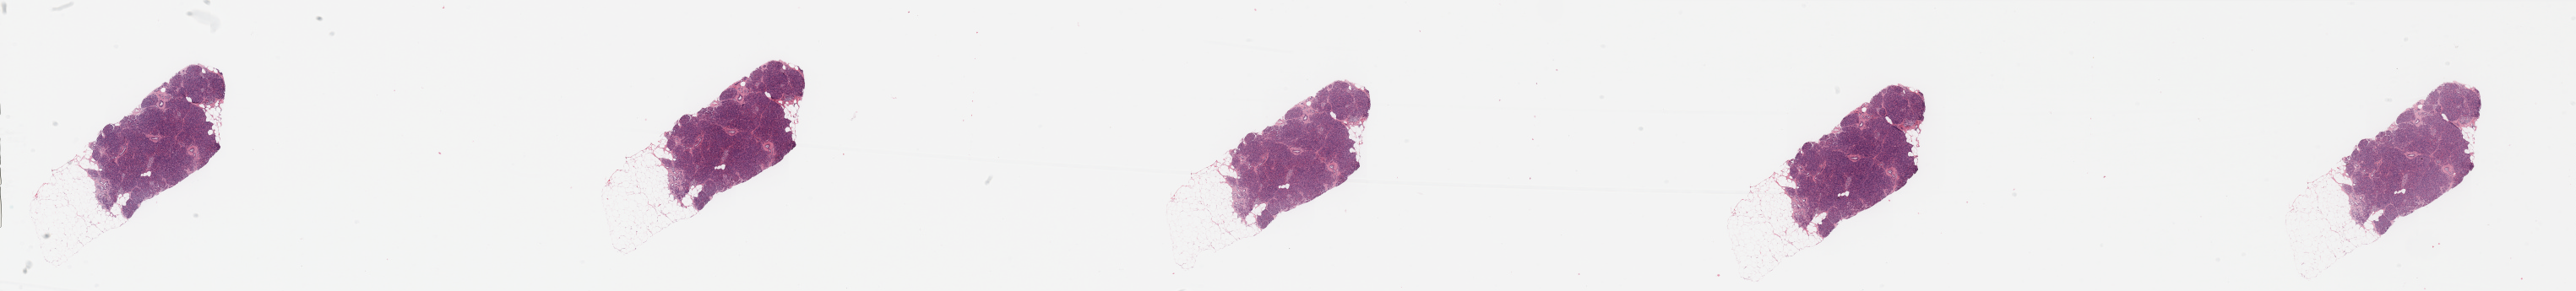
Digitized Hematoxylin and eosin (H&E) stained tissue section (whole slide), shown as a low-resolution overview of the whole scanned area (about 48.2 x 5.5 mm), pancreas, normal (non-tumour) tissue. Patient: male, age 74 years.
- this section: normal (non-tumour) tissue from the same patient
- patient diagnosis: Infiltrating duct carcinoma, NOS